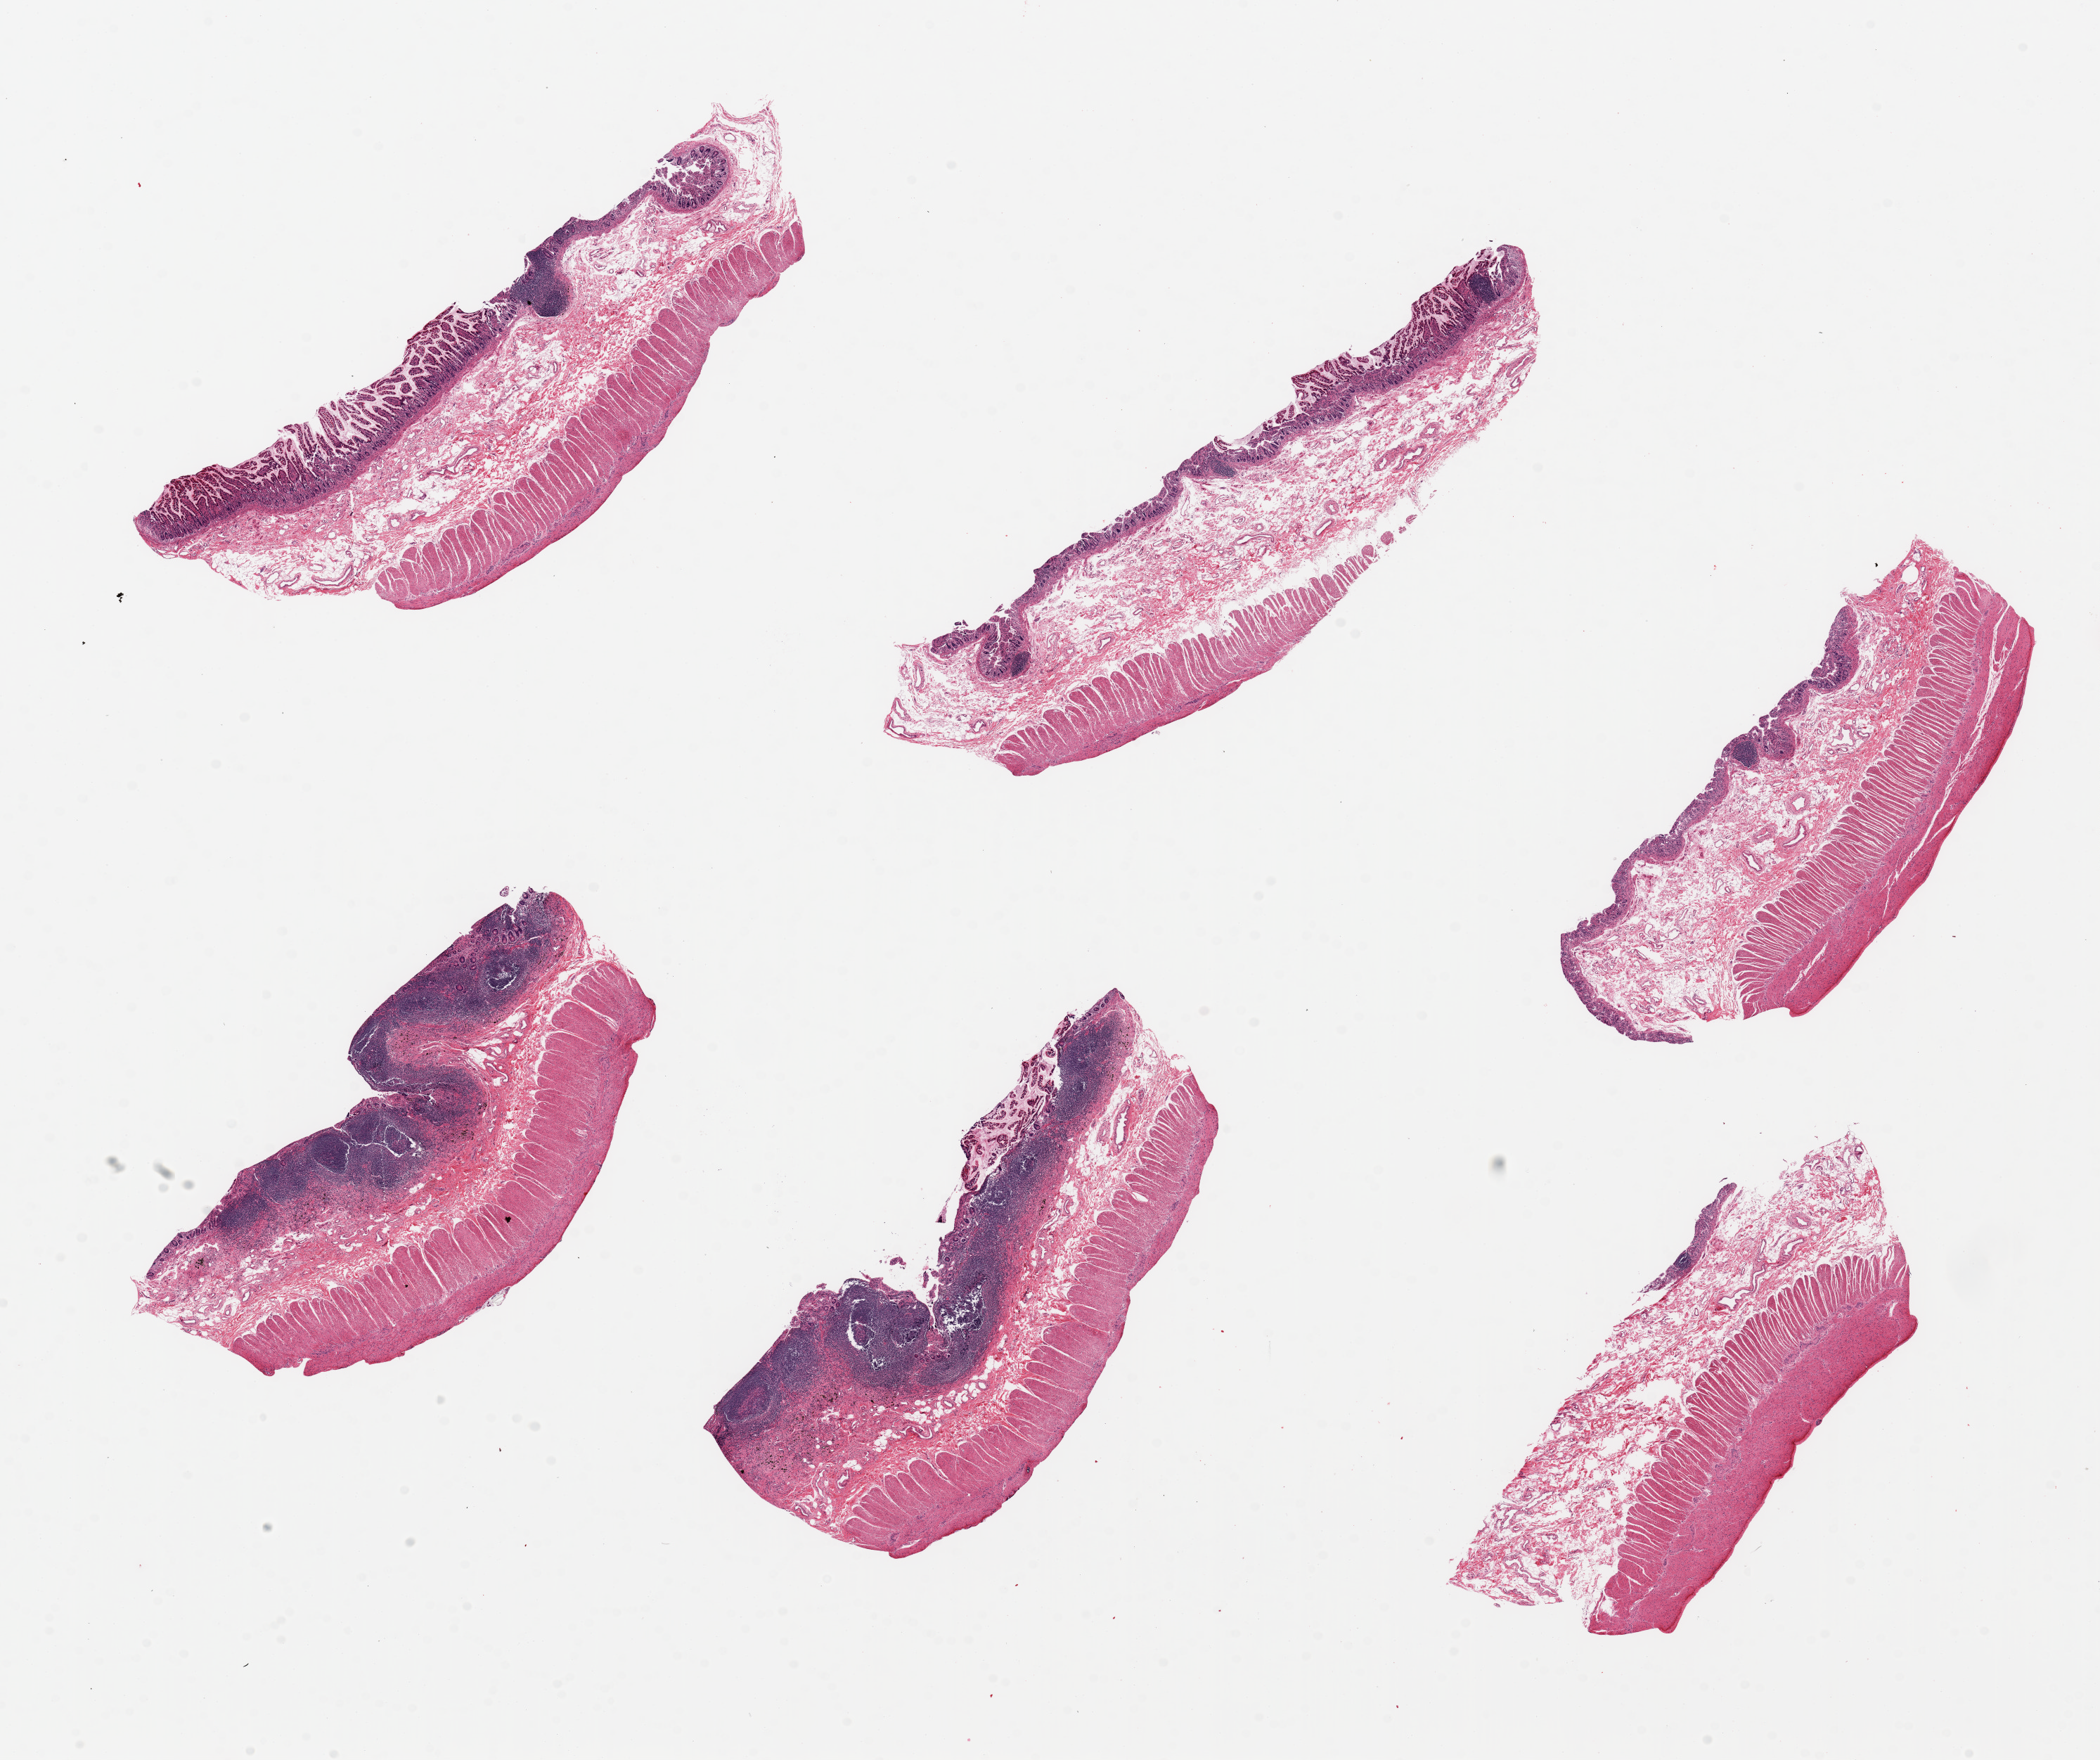
Digitized haematoxylin and eosin-stained section, brightfield — a low-resolution overview of the entire scanned area, about 23.6 x 19.8 mm (acquisition: 20x scan), PAXgene-fixed, paraffin-embedded tissue, section of ileum (target tissue), tissue donor sample. Female donor.
Reviewer comment on this tissue sample: 6 pieces, up to 9x2mm; 2 of 6 have good lymphoid tissue (slightly autolyzed); 3 have focal lymphoid nodules; all have muscle.